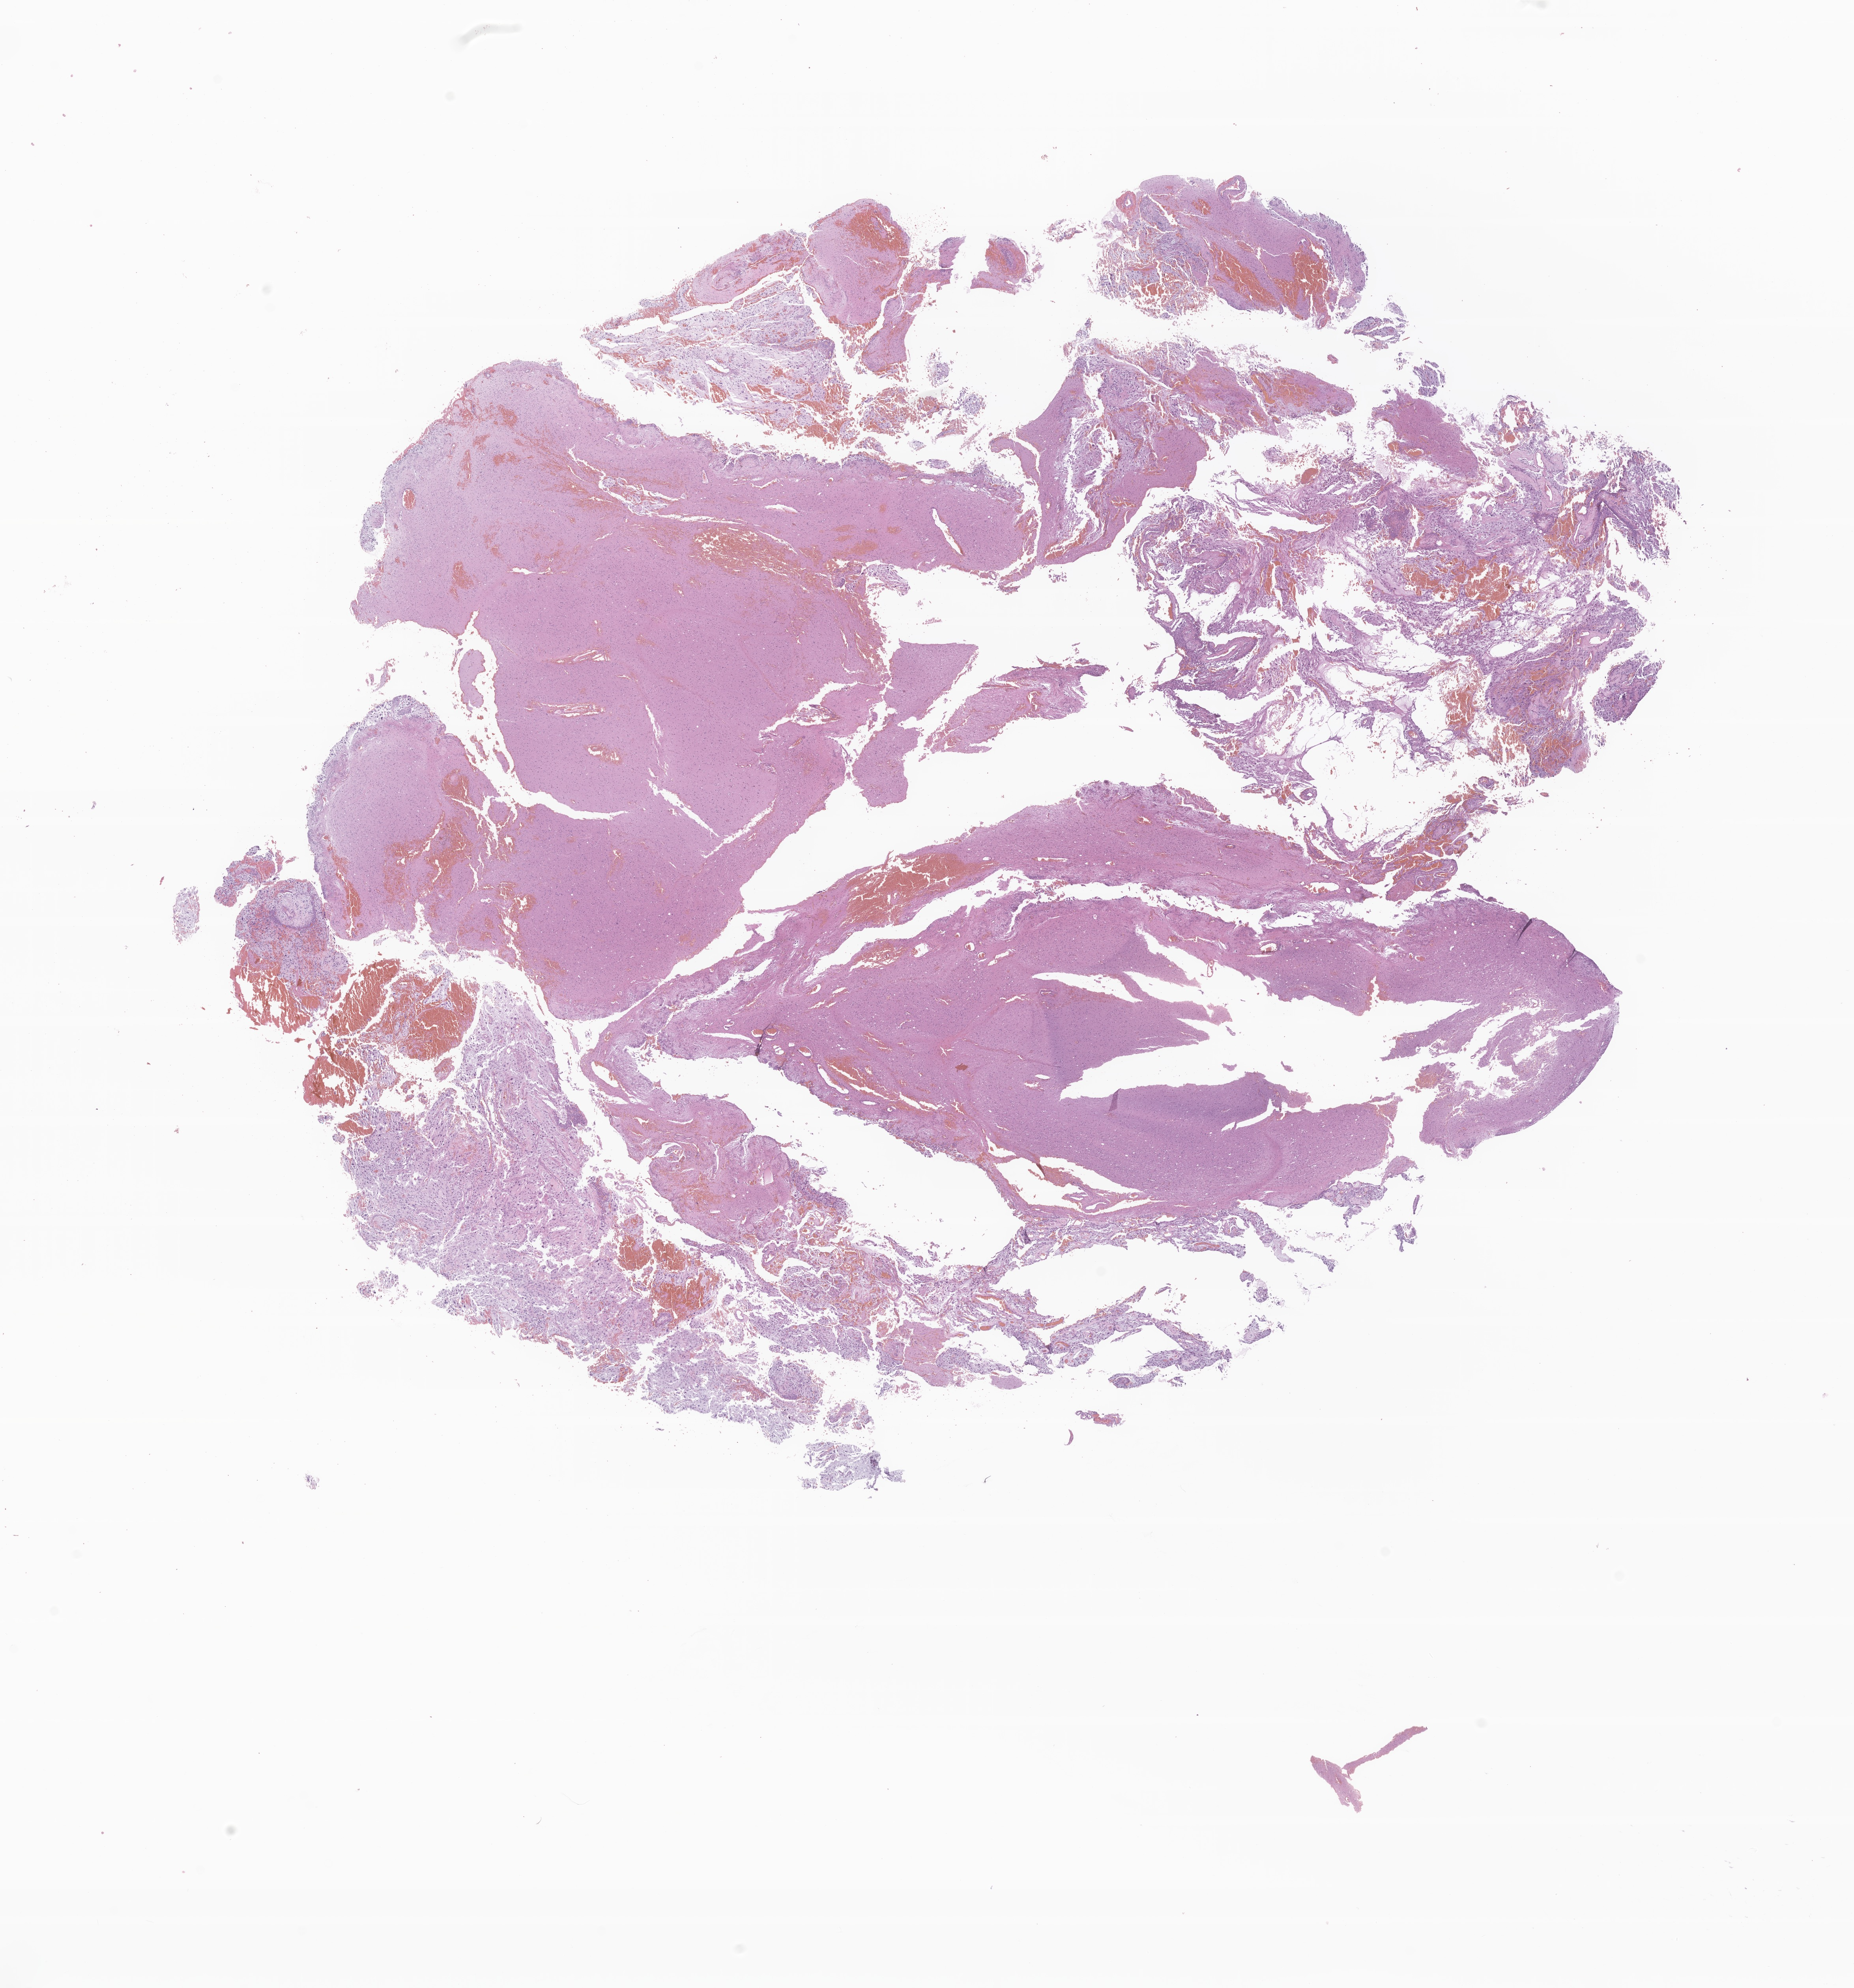
Hematoxylin and eosin (H&E) whole-slide image of tumor tissue from the brain, a low-resolution overview of the entire scanned area, about 19.8 x 21.2 mm, formalin-fixed, paraffin-embedded (FFPE) tissue. Patient male; age 151 months (12 years 7 months).
Diagnosis (ICD-O-3 morphology term): Pilocytic astrocytoma.